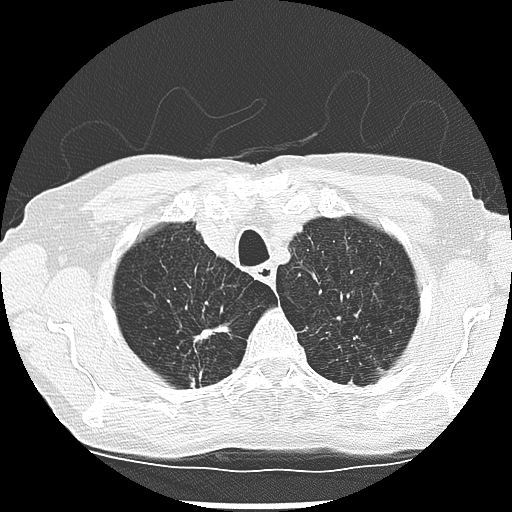
Low-dose screening chest CT, one axial slice. Slice 231 of 265 in the series (ordered by position). Reconstruction kernel LUNG. 120 kVp. Lung window (W 1500 / L -600 HU). 2.5 mm slice thickness. 512 × 512 image matrix, field of view 300 × 300 mm.
Structures marked on this image (expert manual segmentation):
- lesion 2 (tumor, upper lobe of right lung): bounding box <195,329,215,342> (left, top, right, bottom; pixels)